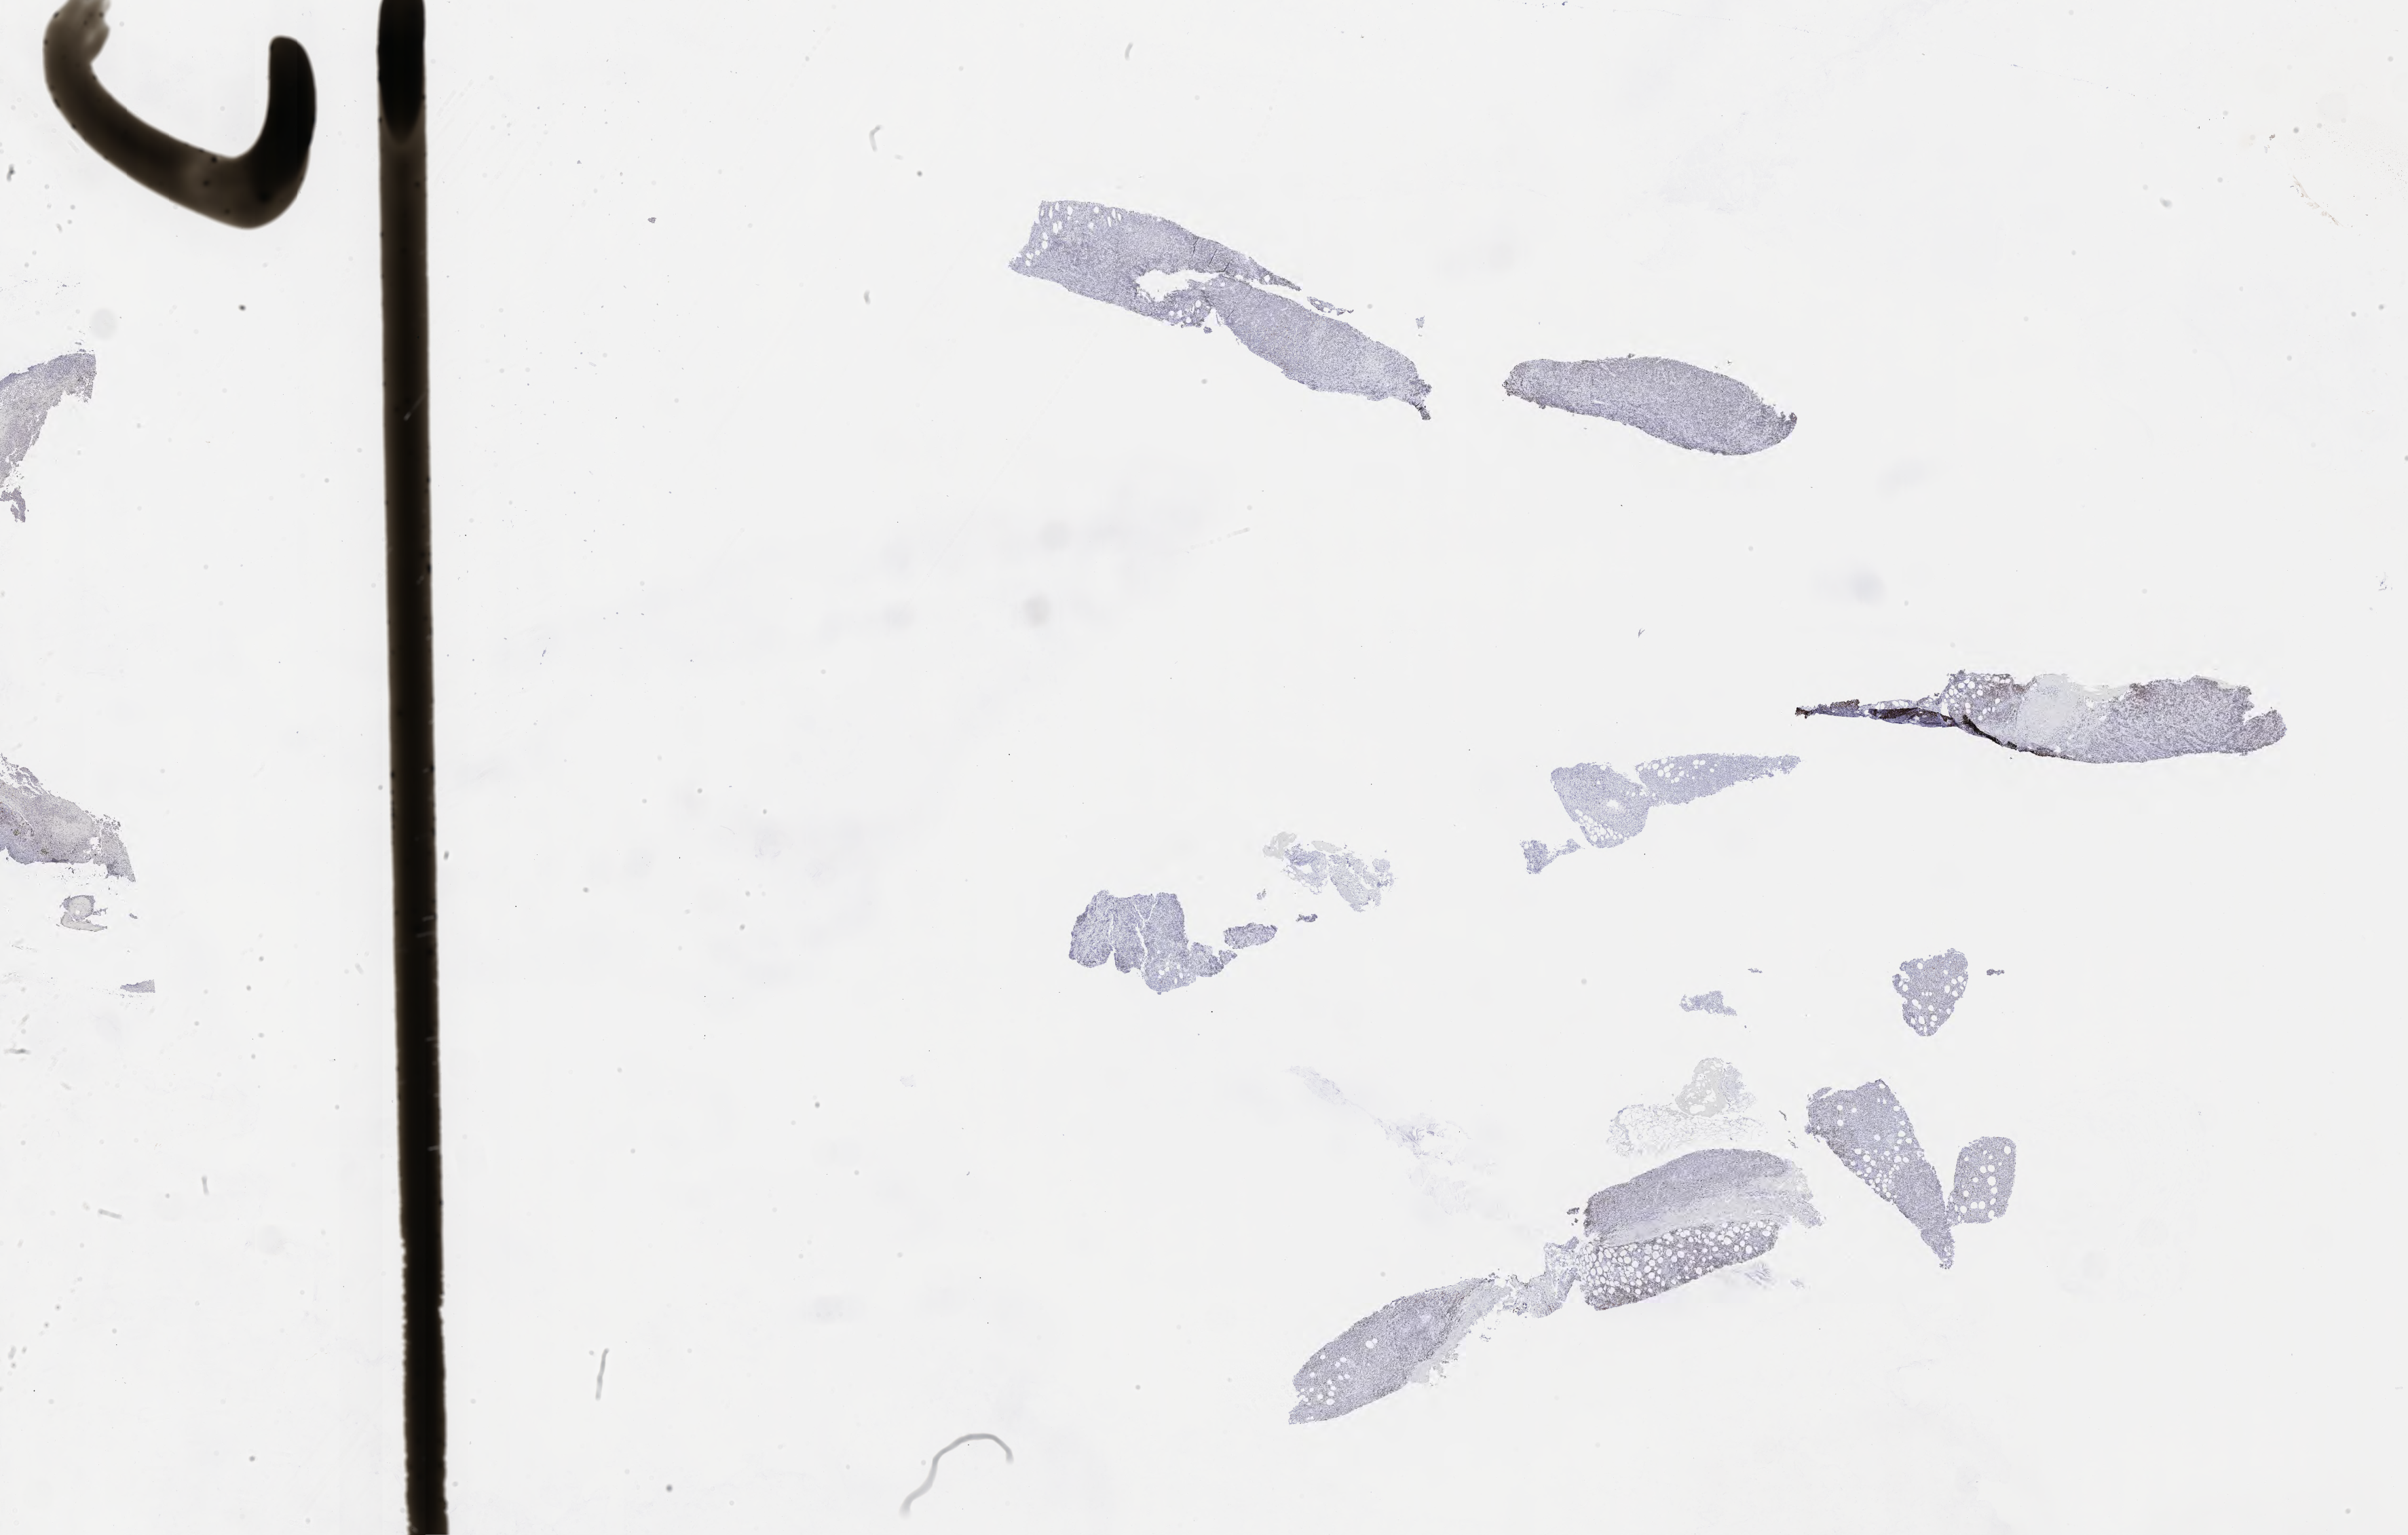
IHC for Ki-67, whole-slide image, whole scanned area (about 28.7 x 18.3 mm) shown as a low-resolution overview. Tumor tissue. Patient: male, age 33 years.
Diagnosis: Burkitt lymphoma, NOS.